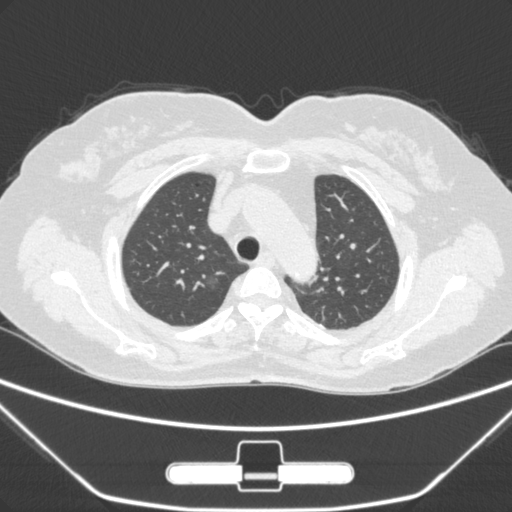
Chest CT, one axial slice. Lung window (W 1500 / L -600 HU). 1 mm slice thickness. 512 × 512 image matrix, field of view 356 × 356 mm. Patient: female, 63 years. From the clinical record (not read from this slice): clinical TNM (as recorded): T1a N0 M0; histopathological grade: G1.
Annotated regions visible in this slice (rectangle marked by the reading radiologist):
- lung tumour (recorded histology: adenocarcinoma): bounding box [x1, y1, x2, y2] px = [201, 275, 231, 305]